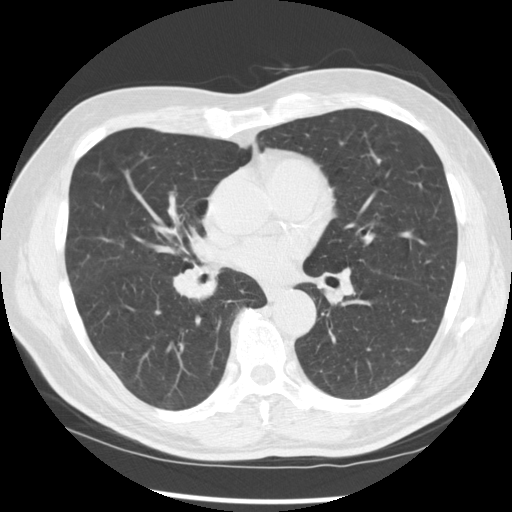
Low-dose screening chest CT, axial slice; baseline screening round; lung window (W 1500 / L -600 HU); 2.5 mm slice thickness; standard (soft-tissue) reconstruction kernel (STANDARD); 120 kVp; 512 × 512 image matrix, field of view 365 × 365 mm. Male participant, aged 67 years at enrolment.
Lesion marked by an expert reader, bounding box <156,246,227,313> (left, top, right, bottom; pixels). The exam's reader record, not a measurement of the box and not confirmed to be the same lesion: non-calcified nodule or mass ≥4 mm, left lower lobe, 15 × 15 mm, spiculated (stellate) margins, soft tissue attenuation. Note: the box lies in the patient's right hemithorax on this image, whereas the reader's record names the left lung; they may be different findings. Later outcome: lung cancer diagnosed 49 days after this screen — squamous cell carcinoma, NOS, right middle lobe, poorly differentiated (G3), stage IIB (AJCC 6th edition), 35 mm at pathology.